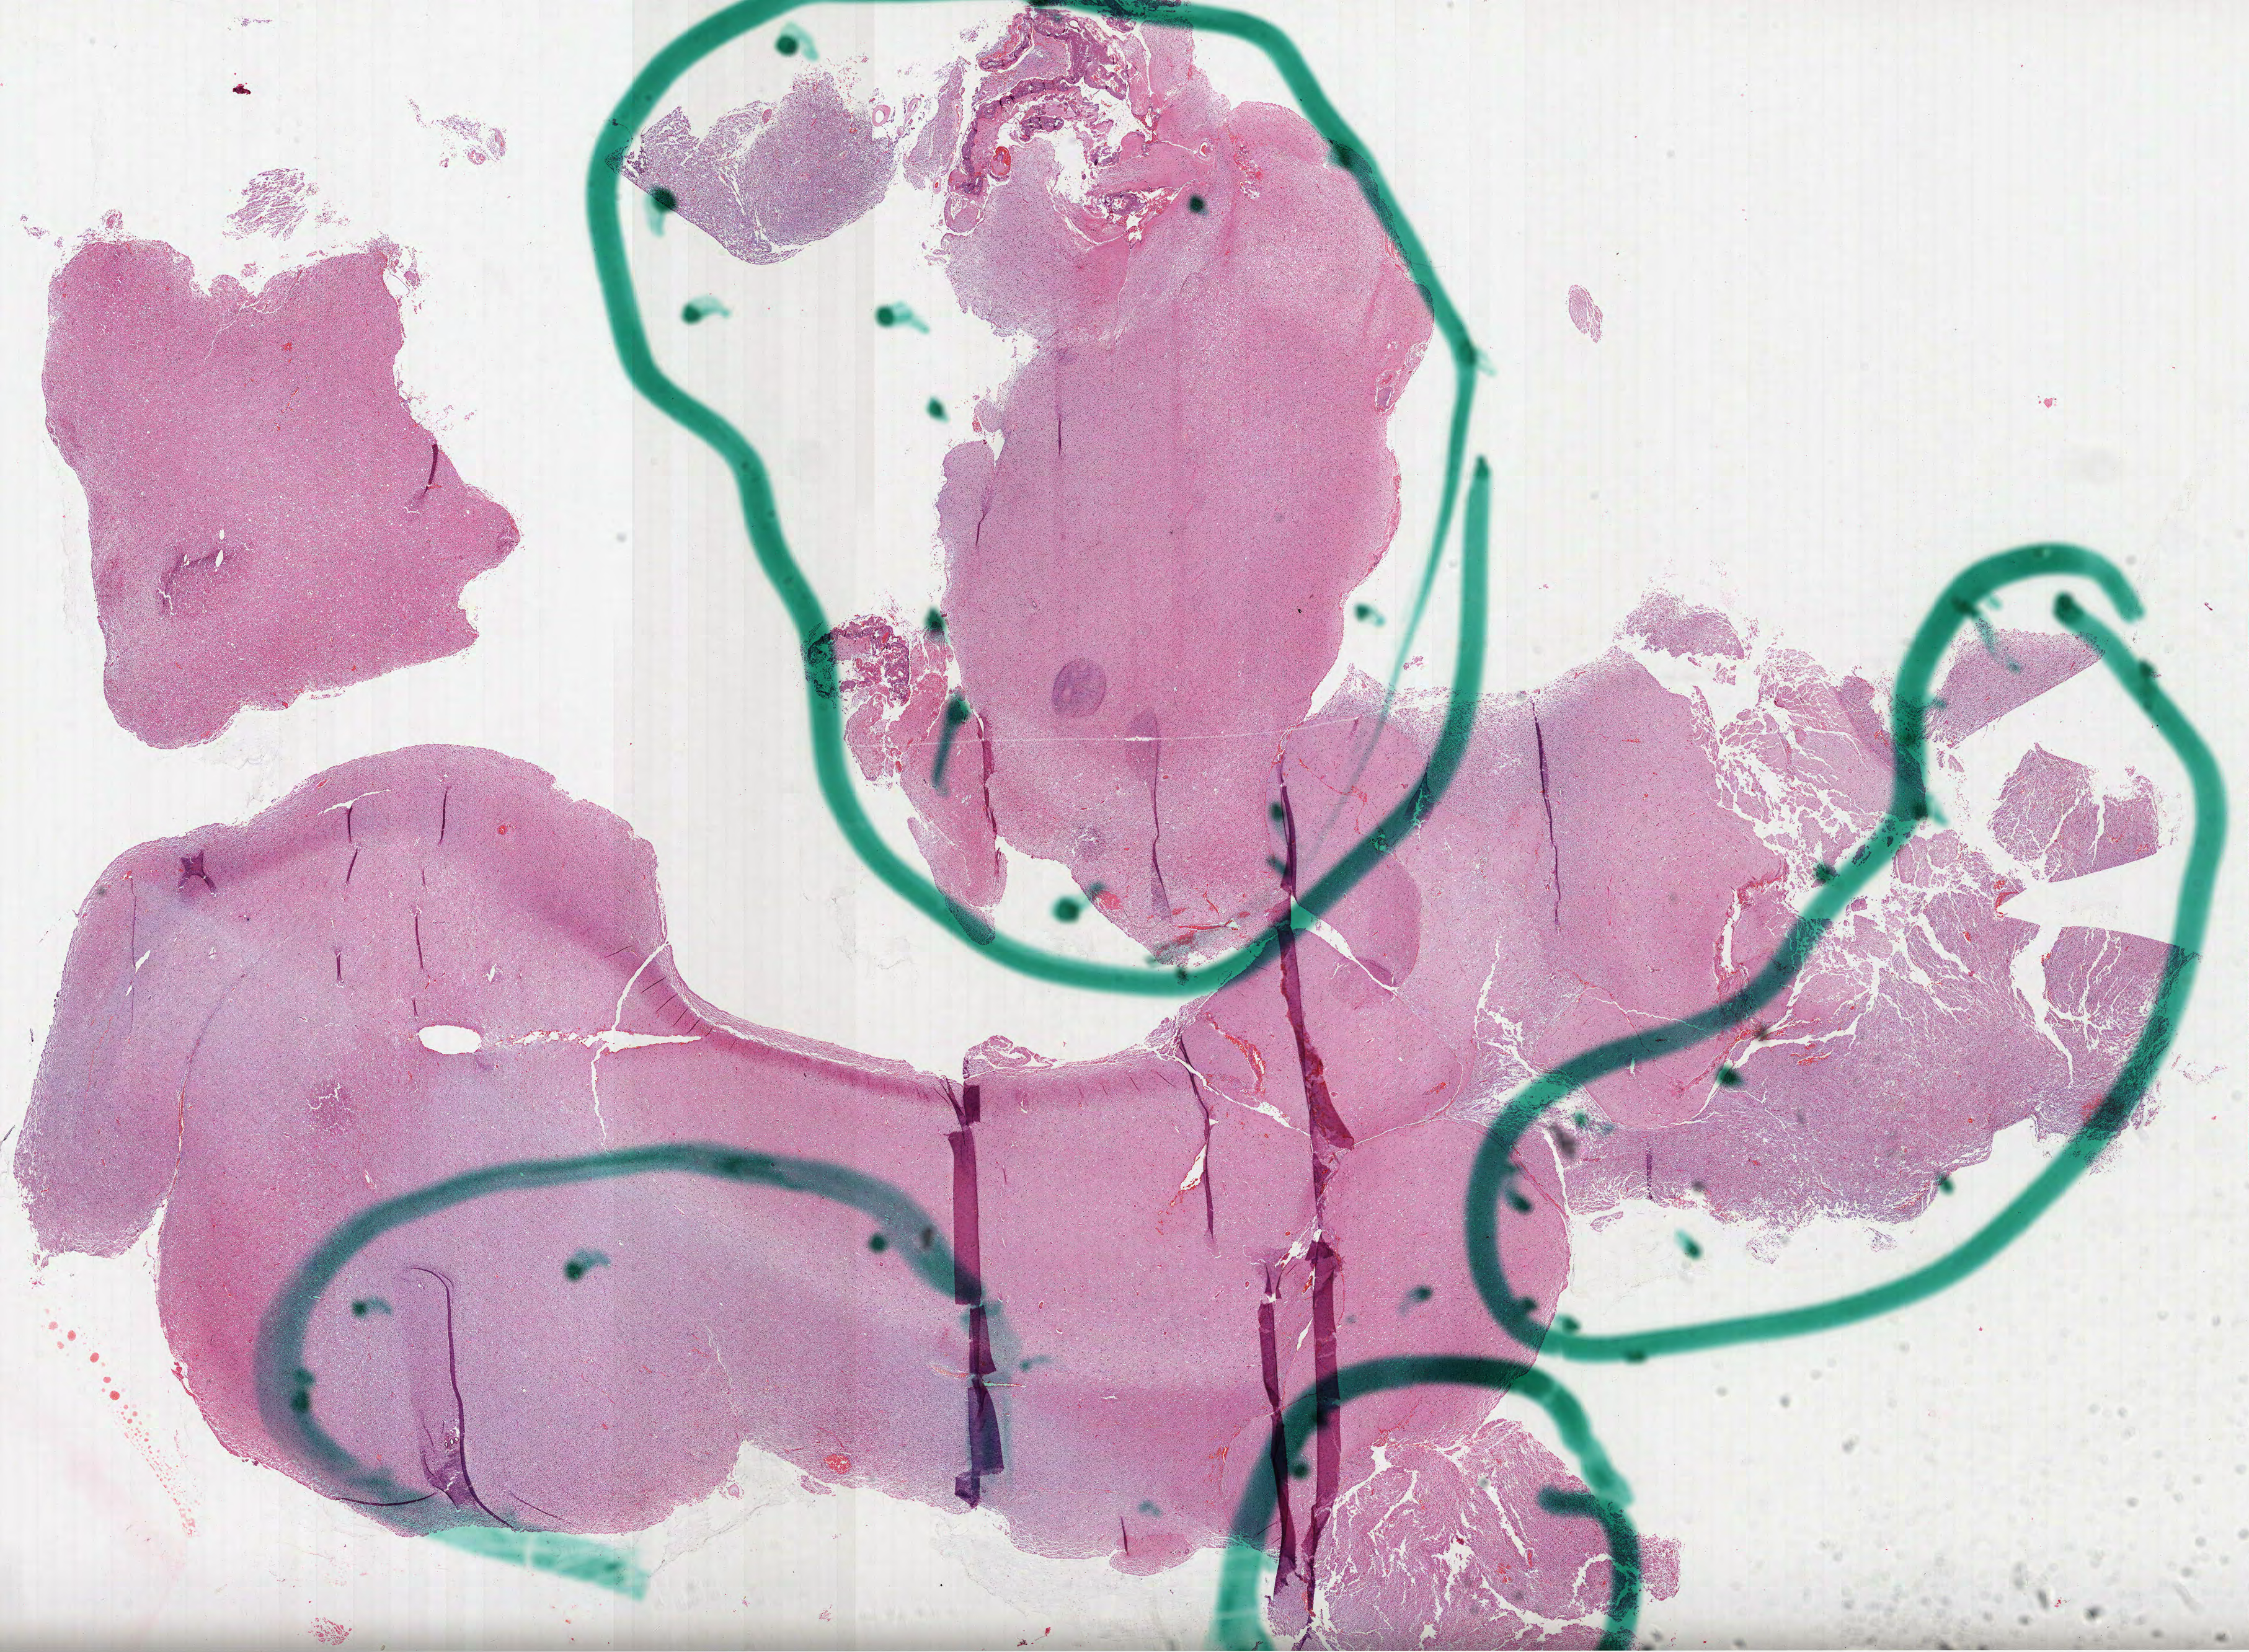
Digitized H&E tissue section (whole slide) — shown as a low-resolution overview of the whole scanned area (about 29.2 x 21.5 mm, from a 40x scan). Formalin-fixed paraffin-embedded (FFPE) diagnostic section. Sample: primary tumour, brain. Male patient; age at initial diagnosis 38 years. Histologic grade: G2 (moderately differentiated).
Histologic diagnosis: Mixed glioma (cerebrum). Laterality: right.